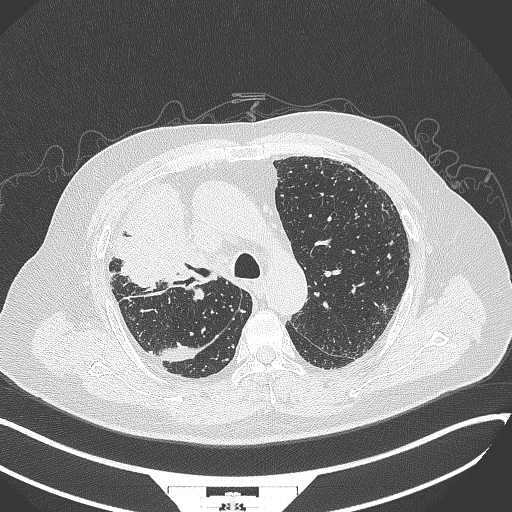
Chest CT, one axial slice; slice 249 of 384 in the series (ordered by position); reconstruction kernel B70f; lung window (W 1500 / L -600 HU); 512 × 512 image matrix, field of view 400 × 400 mm. Male patient, age 69 years. From the clinical record (not read from this slice): clinical TNM (as recorded): T4 N3 M1.
Outlined on this slice (rectangle marked by the reading radiologist):
- lung tumour (recorded histology: adenocarcinoma): bounding box [x1, y1, x2, y2] px = [104, 167, 208, 286]